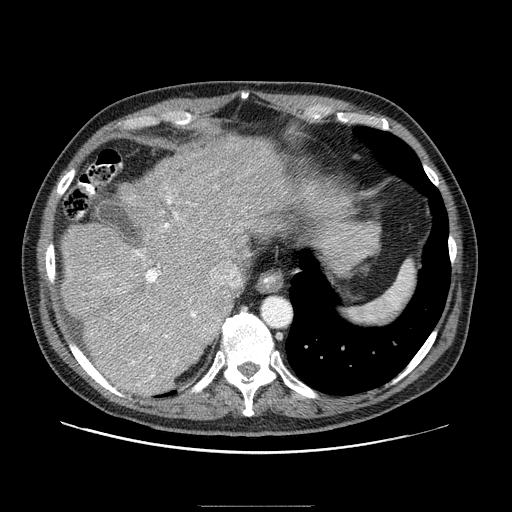
Contrast-enhanced abdominal CT (liver protocol), one axial slice; slice 67 of 99 in the series (ordered by position); reconstruction kernel STANDARD; 100 kVp; one of 2 acquisitions stored at this slice position; soft-tissue window (W 400 / L 40 HU); 2.5 mm slice thickness; 512 × 512 image matrix, field of view 400 × 400 mm. Case-level facts recorded for this patient, not image findings: diagnosis: hepatocellular carcinoma (patient treated with transarterial chemoembolisation; whether this scan precedes or follows treatment is not stated here); TNM stage (as recorded): Stage-II; Child-Pugh class: A; tumour nodularity: multinodular; tumour size: 3.2 cm.
Structures marked on this image (semi-automatic segmentation, software-assisted and operator-edited):
- abdominal aorta: bounding box <263,297,291,326> (left, top, right, bottom; pixels)
- liver parenchyma outside the tumour (the mass and vessels are separate outlines, so this box may not span the whole liver): <60,134,323,394>
- liver vessels: <96,196,215,386>